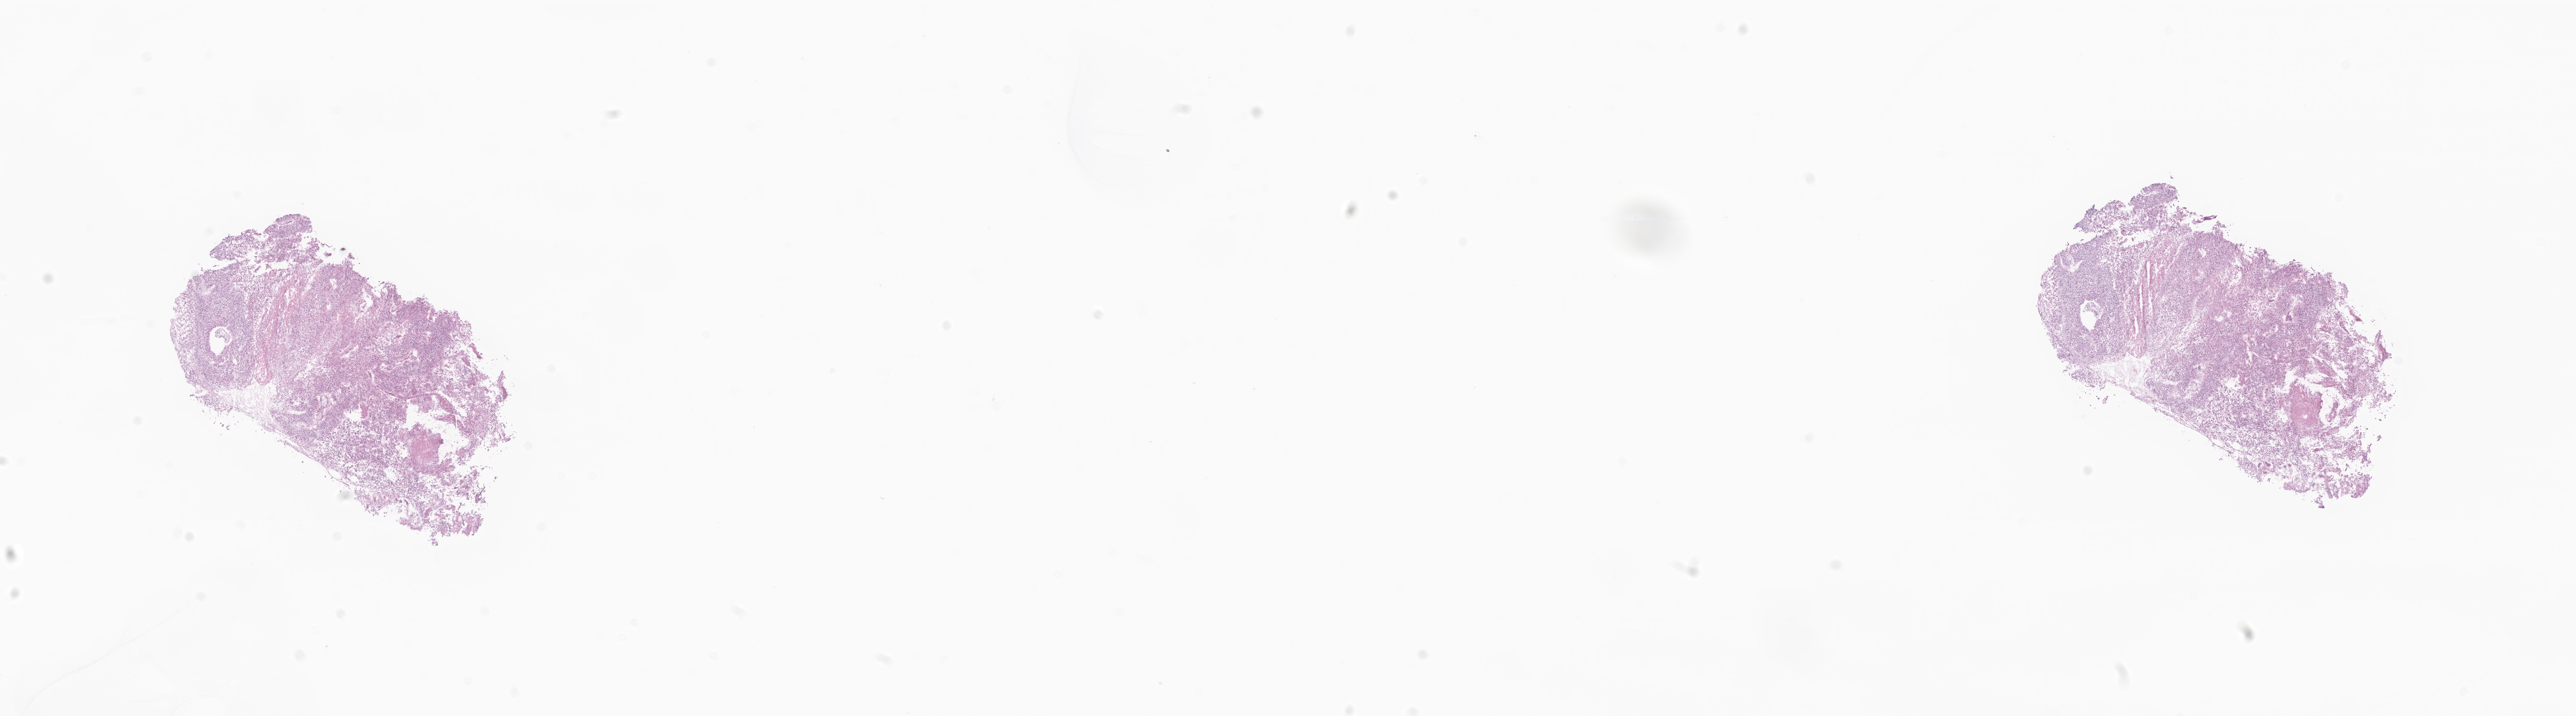
H&E whole-slide image of tumor tissue from the brain, shown as a low-resolution overview of the whole scanned area (about 27.5 x 7.6 mm), frozen section (OCT-embedded). Female patient, age 58 months (4 years 10 months).
Diagnosis (ICD-O-3 morphology term): Neoplasm, uncertain whether benign or malignant.